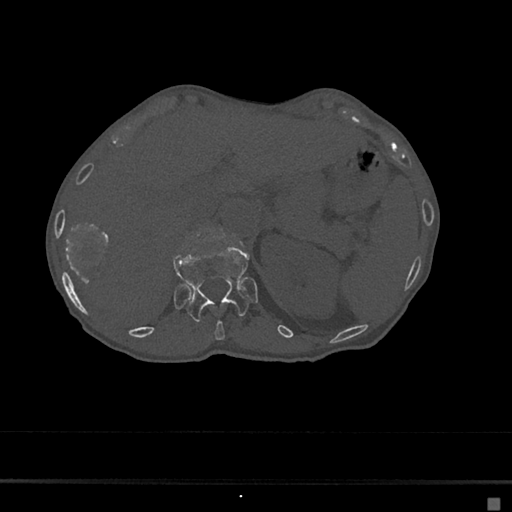
CT including the spine, one axial slice. Position 129 of 797 along the scan axis. 120 kVp. Bone window (W 1800 / L 400 HU). 0.5 mm slice thickness. 512 × 512 image matrix, field of view 360 × 360 mm. Patient: female, 68 years. From the clinical record (not read from this slice): primary cancer: renal.
Outlined on this slice (semi-automatically segmented with operator editing):
- T11 vertebra: bounding box [x1, y1, x2, y2] px = [215, 320, 225, 341]
- T12 vertebra: [173, 246, 248, 322]